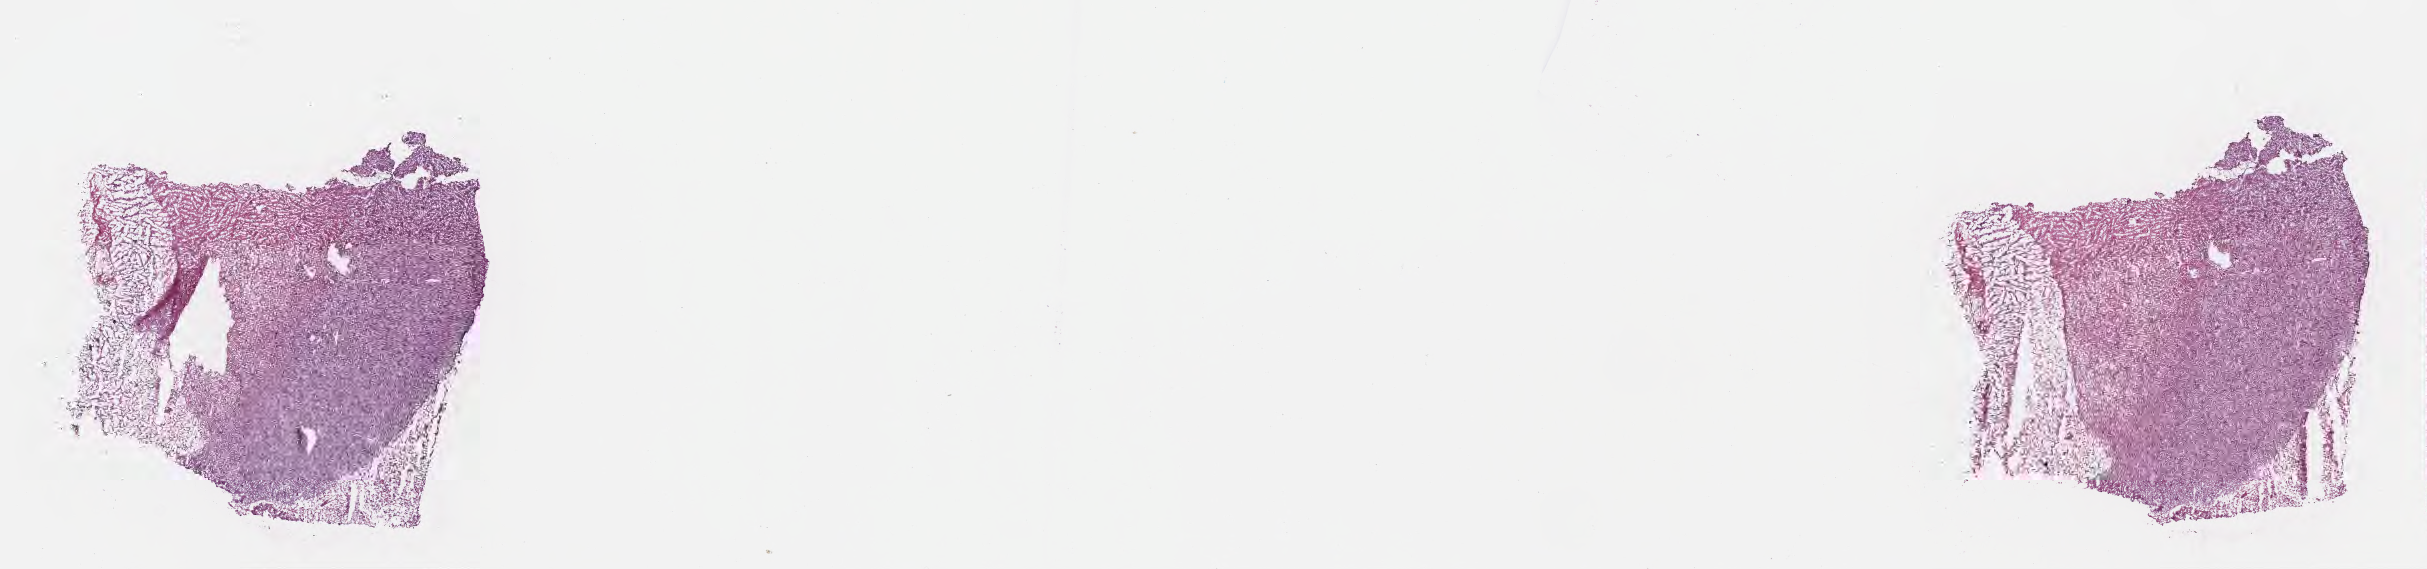
Haematoxylin and eosin whole-slide image, low-resolution overview of the scanned area, about 19.6 x 4.6 mm; frozen section (tissue freezing medium); primary tumor; anatomic site: brain. Male, age 45 years at initial diagnosis. Pathologist review of this section (percent, as recorded): tumor cells 17%, tumor nuclei 53%, stromal cells 55%, necrosis 13%, normal cells 15%. Inflammatory infiltration, as recorded: lymphocyte infiltration 0%, monocyte infiltration 0%, neutrophil infiltration 0%.
Histologic diagnosis: Glioblastoma, NOS. Section: bottom of the tissue portion.